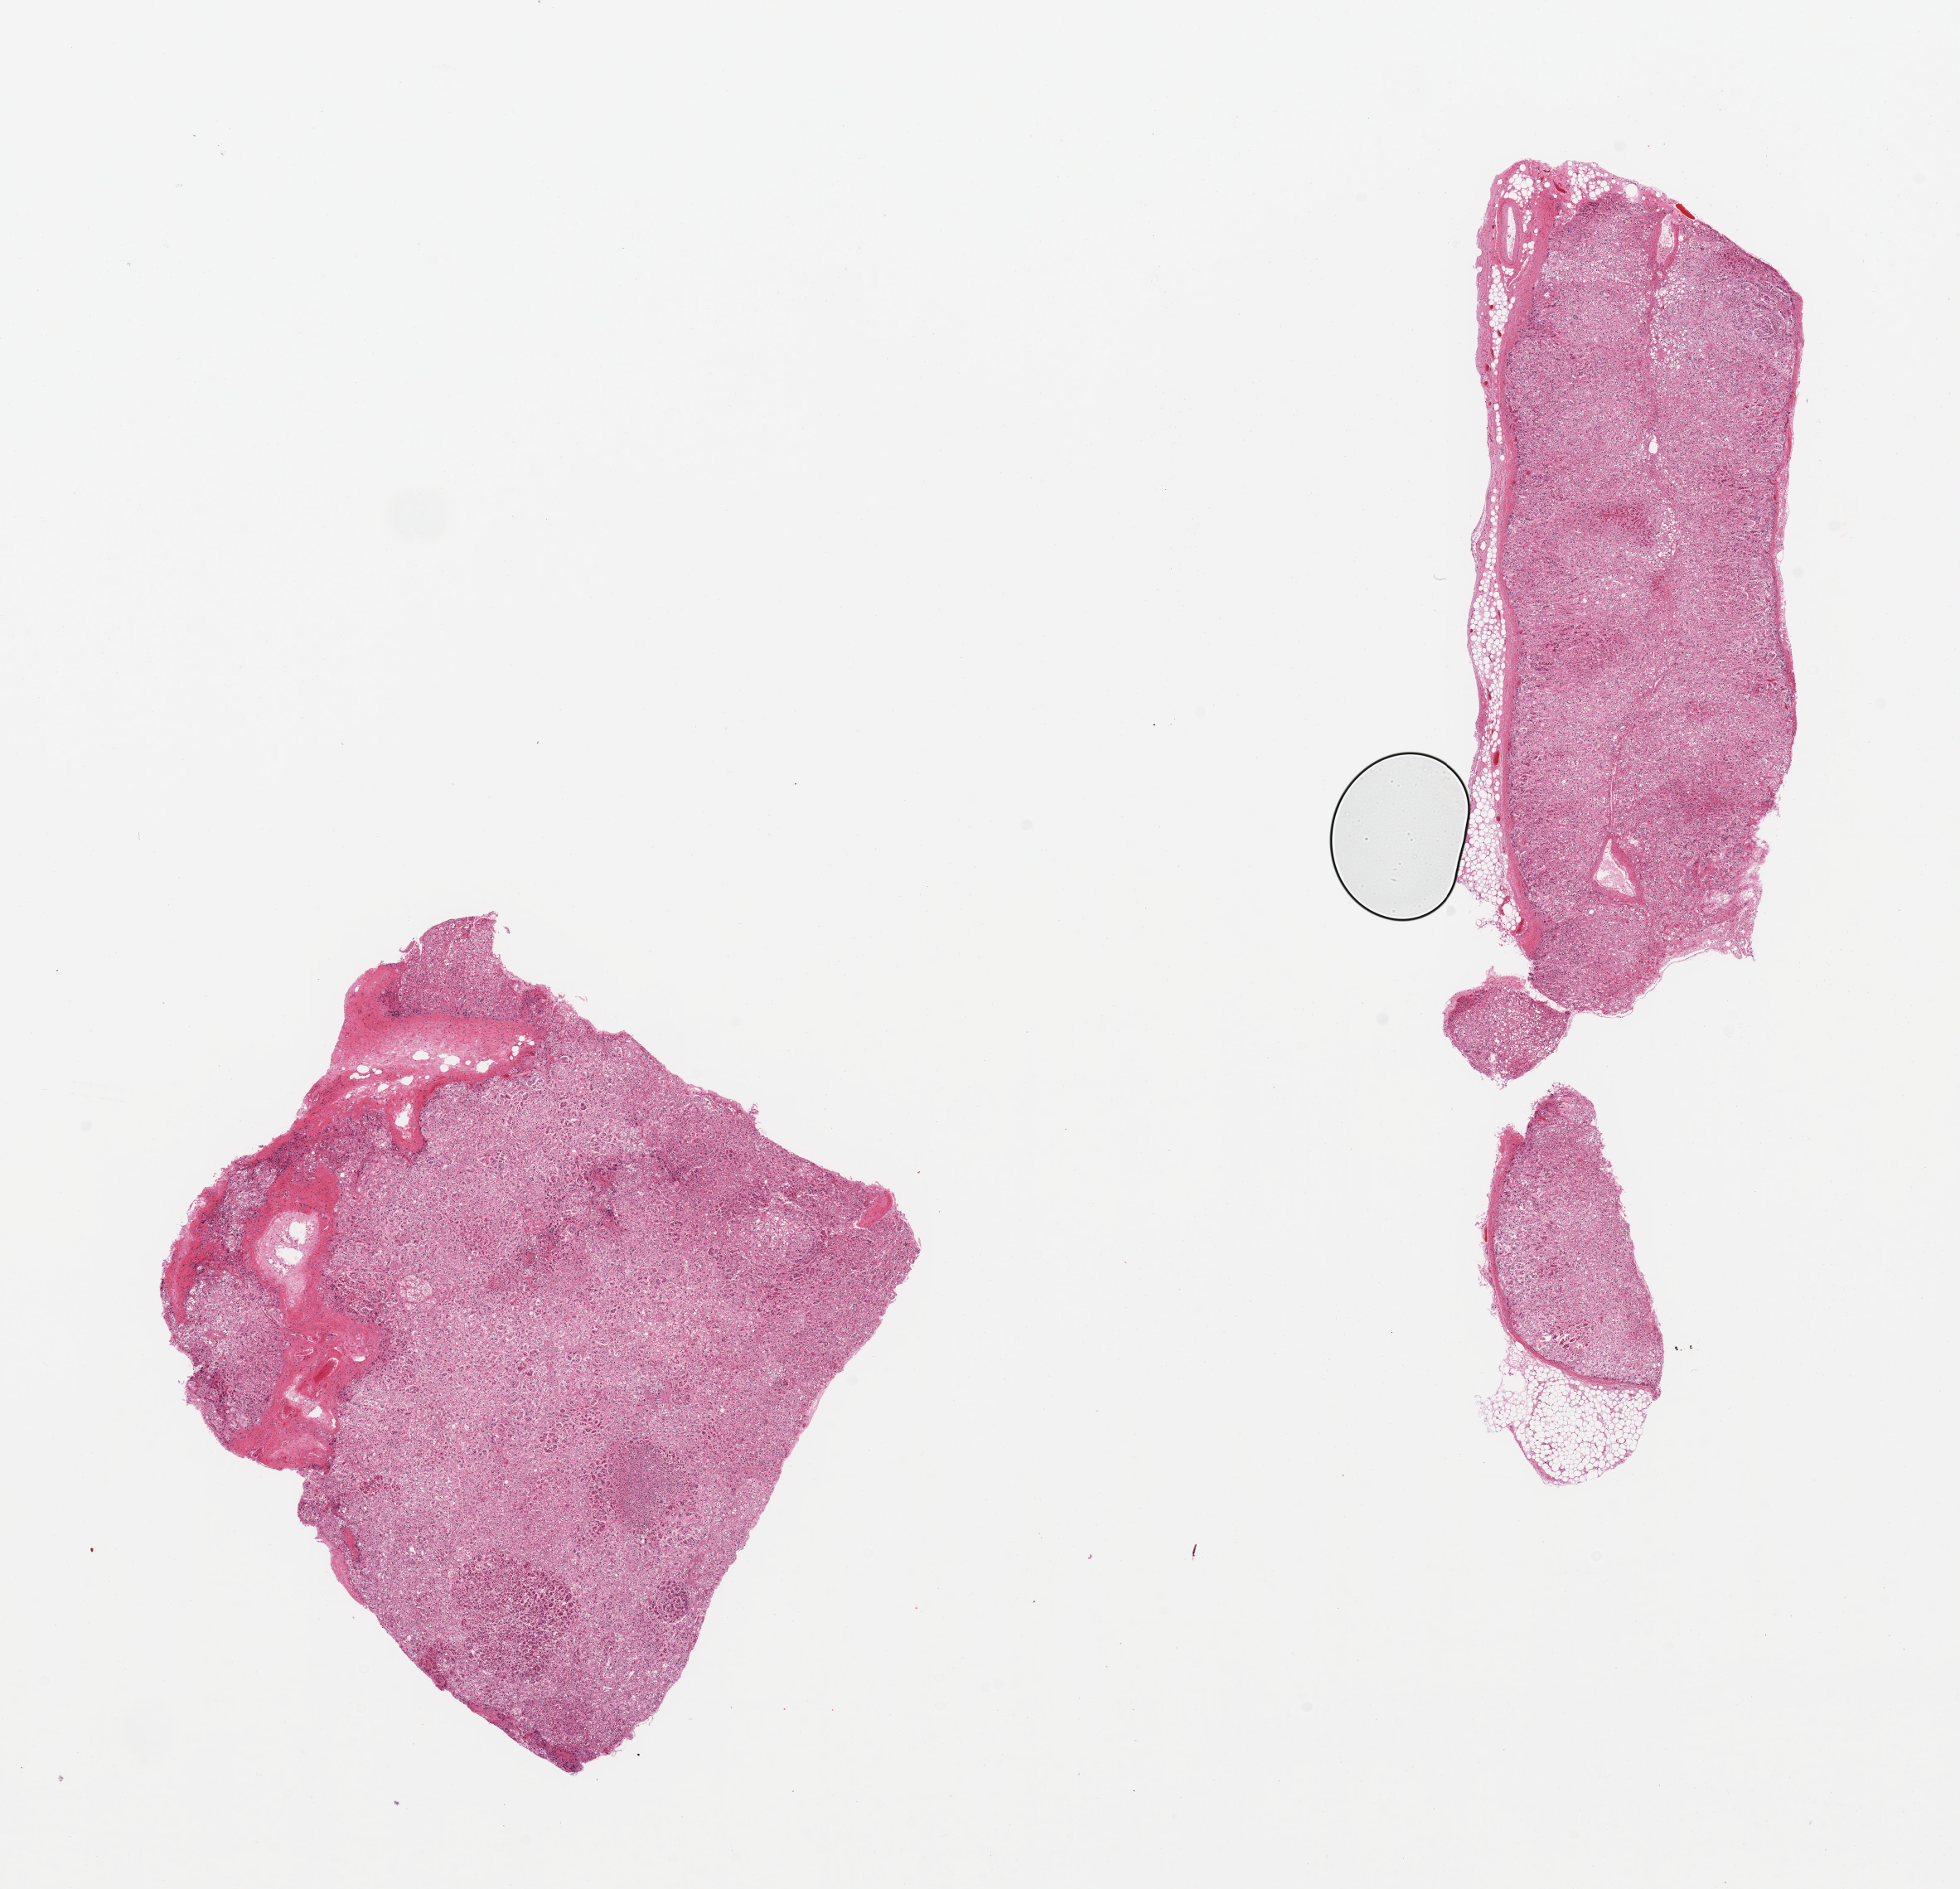
Whole-slide image, haematoxylin and eosin stain, a low-resolution overview of the entire scanned area, about 18.7 x 18.0 mm (acquisition: 20x scan). PAXgene-fixed paraffin-embedded (PFPE) section. Section of adrenal gland (target tissue). Tissue donor sample. Donor sex: male.
Pathologist's review note for this sample: 2 pieces; well dissected; 10% external fat.